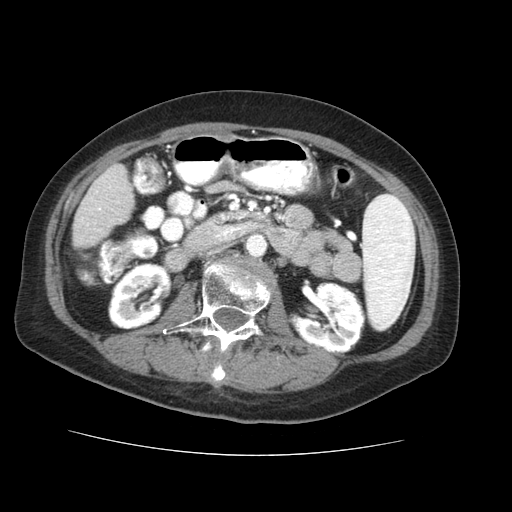
Contrast-enhanced abdominal CT (liver protocol), one axial slice; slice 9 of 73 in the series (ordered by position); soft-tissue window (W 400 / L 40 HU); 2.5 mm slice thickness; 512 × 512 image matrix. Case-level facts recorded for this patient, not image findings: diagnosis: hepatocellular carcinoma (patient treated with transarterial chemoembolisation; whether this scan precedes or follows treatment is not stated here); TNM stage (as recorded): Stage-IVB; Child-Pugh class: A; tumour differentiation: well differentiated; tumour nodularity: uninodular.
Annotated regions visible in this slice (semi-automatically segmented with operator editing):
- liver parenchyma outside the tumour (the mass and vessels are separate outlines, so this box may not span the whole liver): bounding box <72,164,126,248> (left, top, right, bottom; pixels)
- liver vessels: <98,229,100,231>